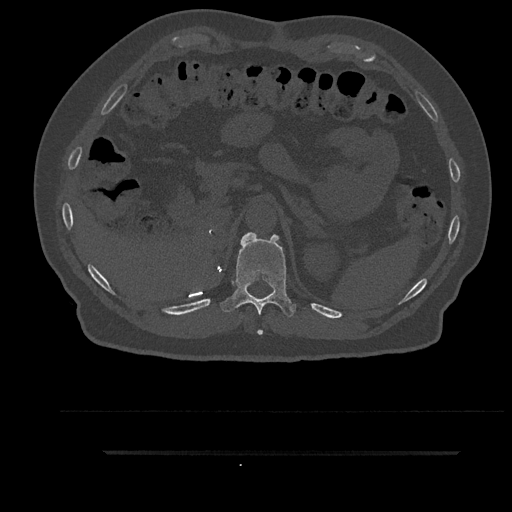
CT including the spine, one axial slice. Position 304 of 797 along the scan axis. Reconstruction kernel Br40s/3. 120 kVp. Bone window (W 1800 / L 400 HU). 0.5 mm slice thickness. 512 × 512 image matrix. Patient: male, 63 years. From the clinical record (not read from this slice): primary cancer: renal; vertebrae with lytic lesions (as recorded): T8.
Outlined on this slice (semi-automatic segmentation, software-assisted and operator-edited):
- T11 vertebra: bounding box (x1, y1, x2, y2) in pixels: (220, 232, 296, 335)